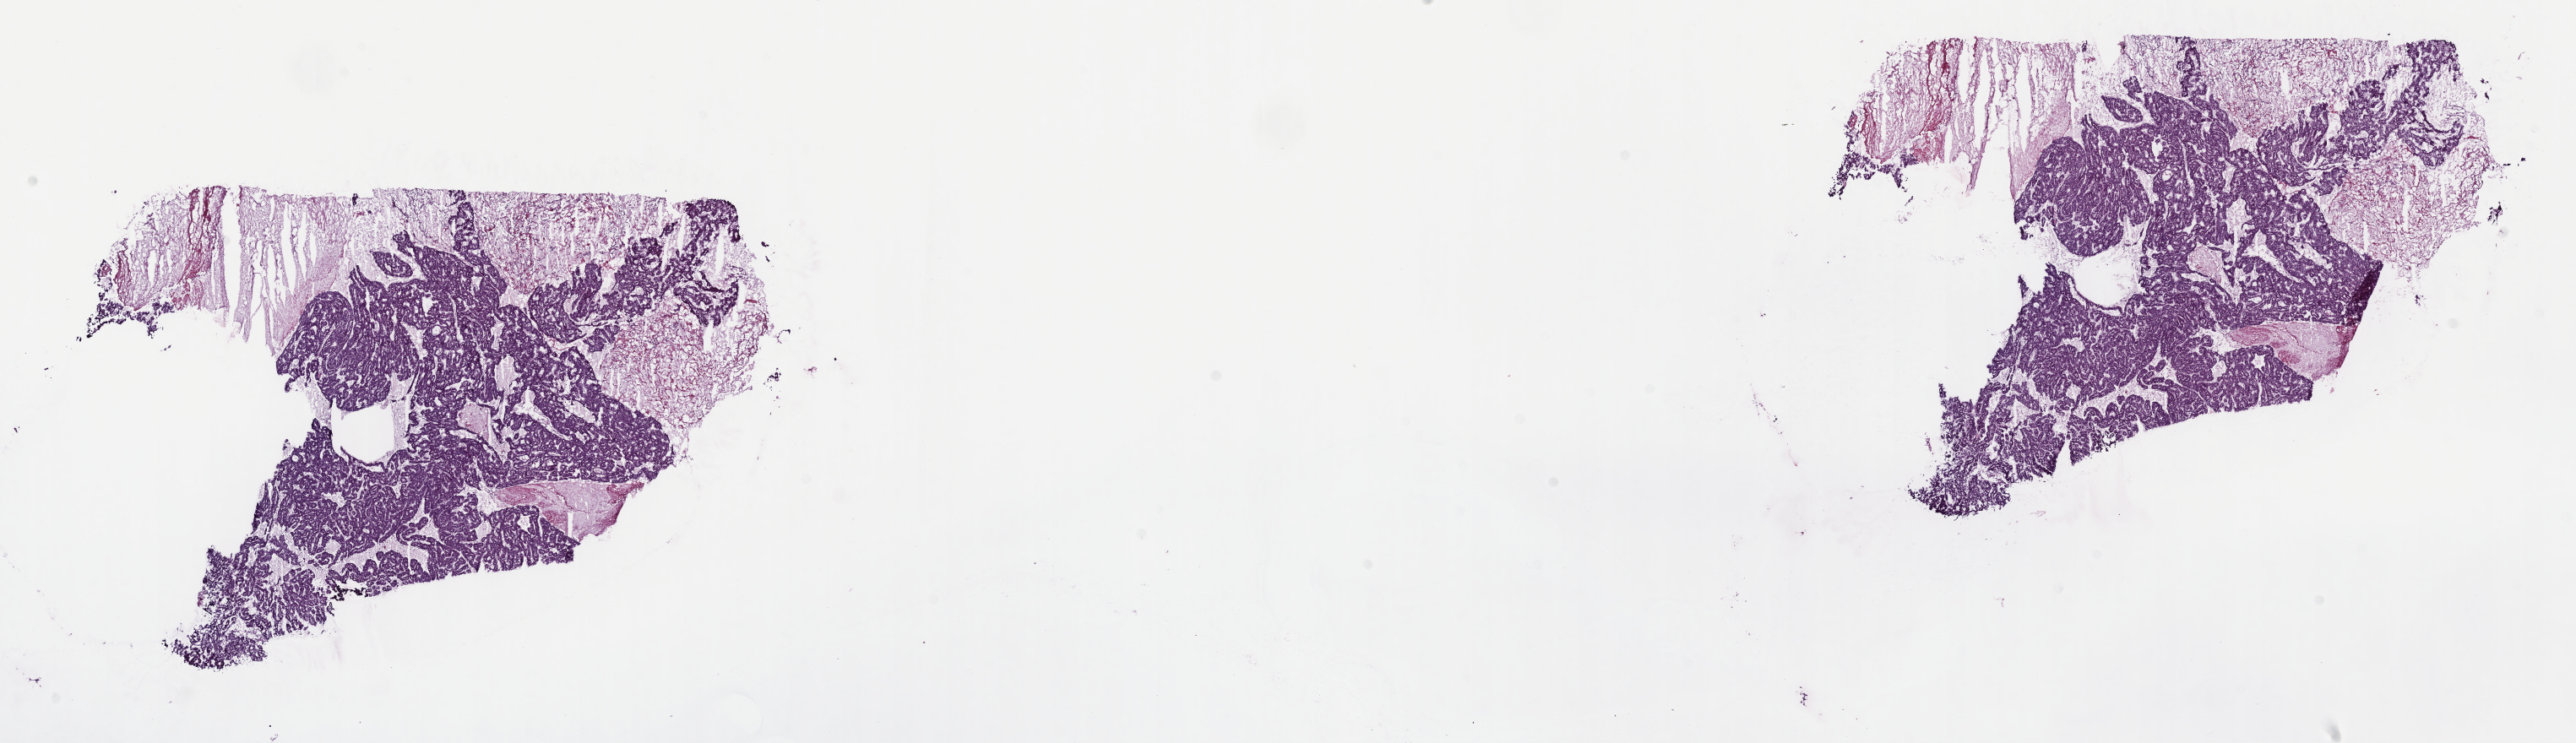
Whole-slide histology image, H&E, shown as a low-resolution overview of the whole scanned area (about 24.7 x 7.1 mm, acquisition: 40x scan), frozen section from the top of the tissue portion, sample: primary tumour, liver. Patient: male, age at initial diagnosis 68 years. Histologic grade: G3 (poorly differentiated). Composition of this section per pathologist review: tumour cells 60%, tumour nuclei 80%, normal cells 0%, stromal cells 40%, necrosis 0%. Infiltration values recorded for this section: lymphocyte infiltration 0%, monocyte infiltration 0%, neutrophil infiltration 0%.
AJCC pathologic stage: I (6th edition). Diagnosis: Hepatocellular carcinoma, NOS.